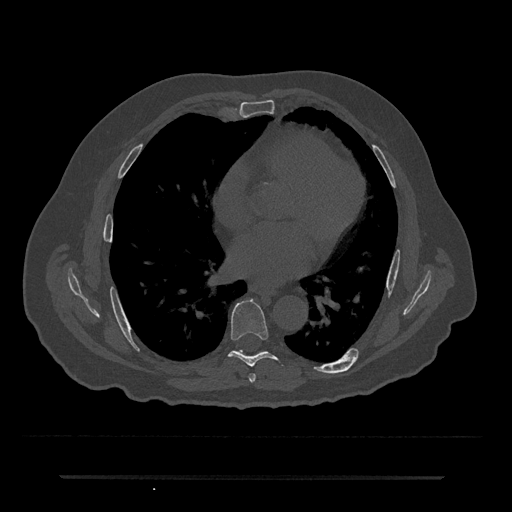
CT including the spine, one axial slice; slice 380 of 797 in the series (ordered by position); reconstruction kernel Br40s/3; bone window (W 1800 / L 400 HU); 0.5 mm slice thickness; 512 × 512 image matrix, field of view 437 × 437 mm. Male patient, age 69 years. From the clinical record (not read from this slice): primary cancer: prostate.
Structures marked on this image (semi-automatically segmented with operator editing):
- T6 vertebra: bounding box [x1, y1, x2, y2] px = [249, 373, 256, 382]
- T7 vertebra: [229, 299, 285, 367]